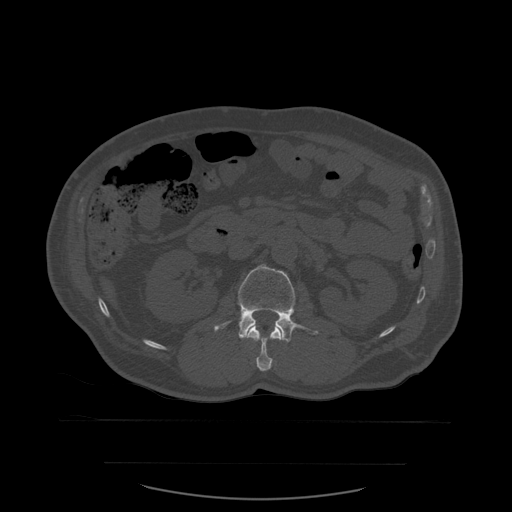
CT including the spine, one axial slice; position 229 of 590 along the scan axis; bone window (W 1800 / L 400 HU); 512 × 512 image matrix, field of view 479 × 479 mm. Patient age 71 years. From the clinical record (not read from this slice): primary cancer: lung; vertebrae with lytic lesions (as recorded): T1, T2, L5, S1.
Annotated regions visible in this slice (semi-automatically segmented with operator editing):
- L1 vertebra: bounding box [x1, y1, x2, y2] px = [247, 326, 282, 372]
- L2 vertebra: [214, 264, 319, 343]